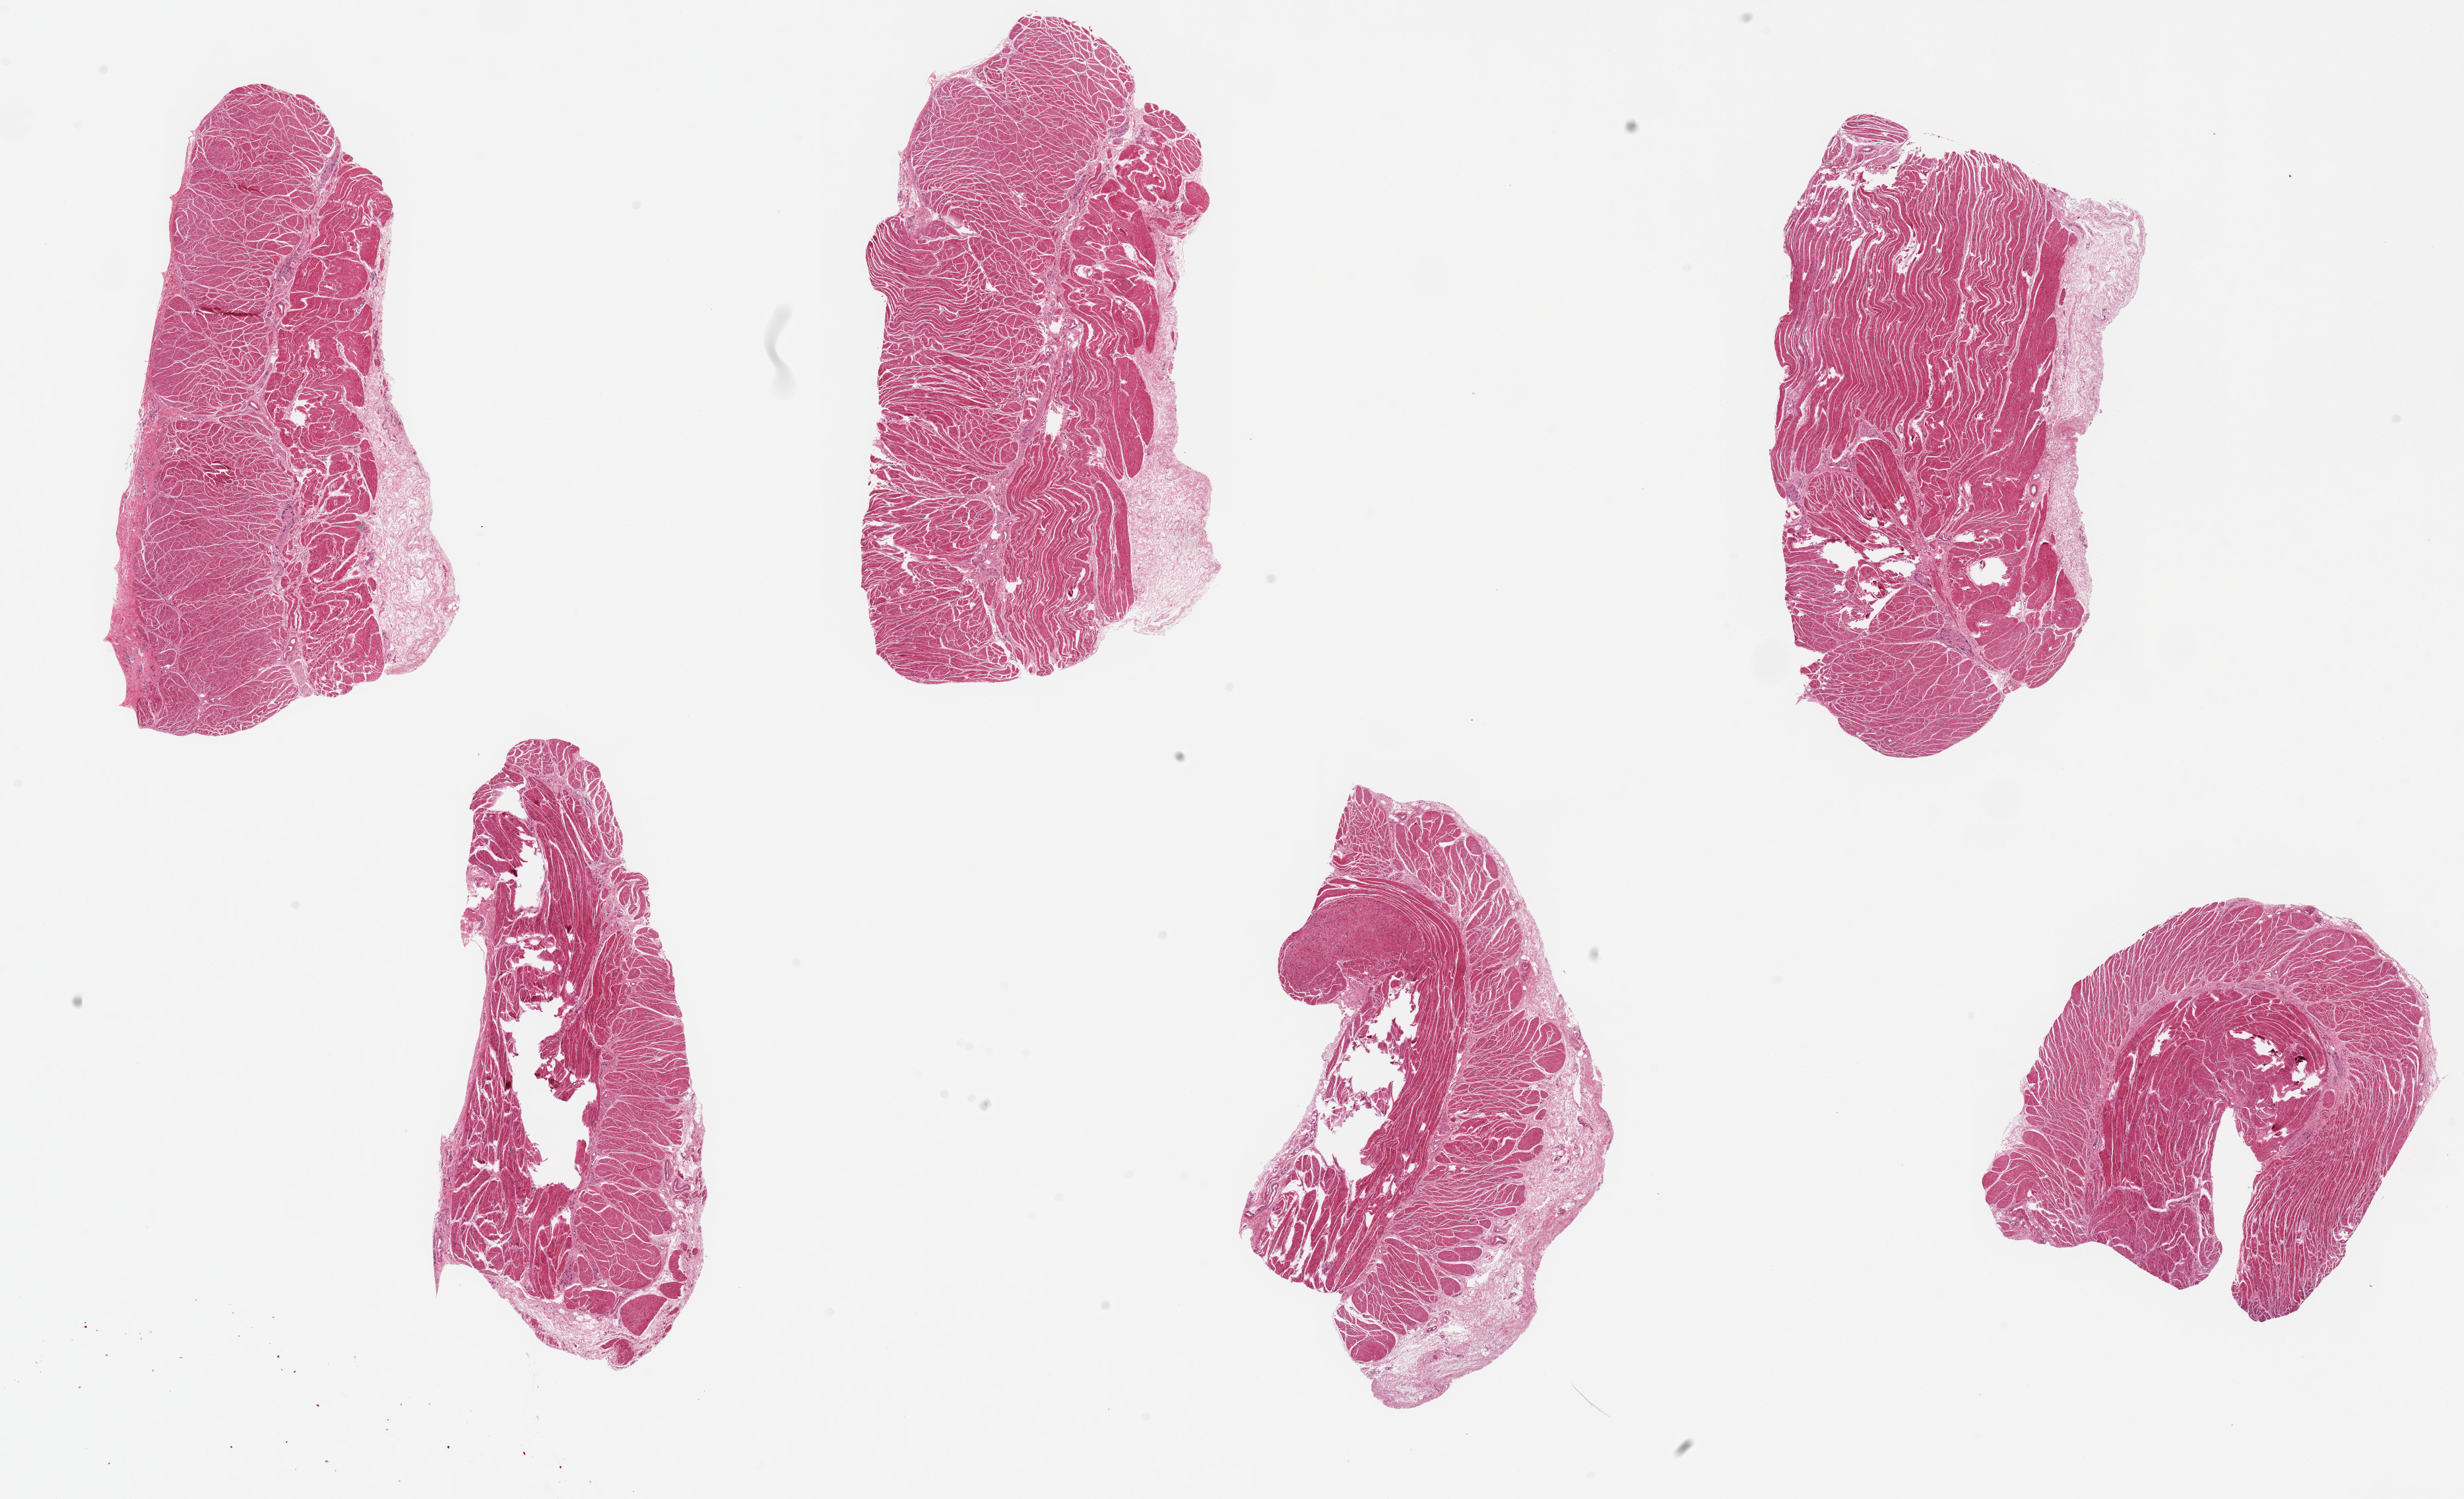
Haematoxylin and eosin whole-slide image, shown as a low-resolution overview of the whole scanned area (about 29.5 x 18.0 mm, slide scanned at 20x). PAXgene-fixed, paraffin-embedded tissue. Sampled site (target tissue): gastroesophageal junction. Donor tissue sample. Donor sex: male.
Reviewer comment on this tissue sample: 6 pieces, up to 8x4mm; all muscularis; good specimens.